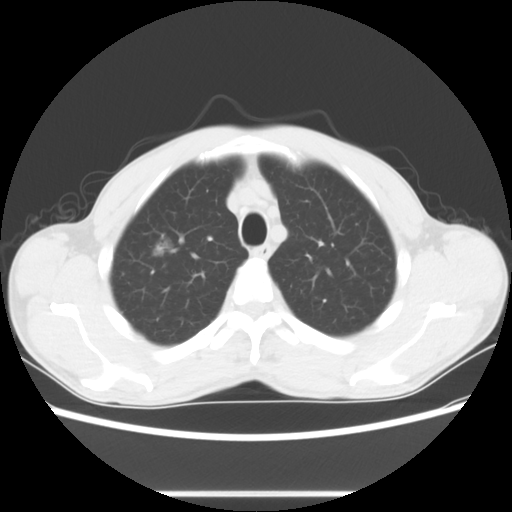
Chest CT, one axial slice; slice 61 of 76 in the series (ordered by position); lung window (W 1500 / L -600 HU); 512 × 512 image matrix, field of view 357 × 357 mm. Patient: male, 54 years. Case-level facts recorded for this patient, not image findings: clinical TNM (as recorded): T1a N0 M0.
Structures marked on this image (rectangle marked by the reading radiologist):
- lung tumour (recorded histology: adenocarcinoma): bounding box <142,228,178,259> (left, top, right, bottom; pixels)